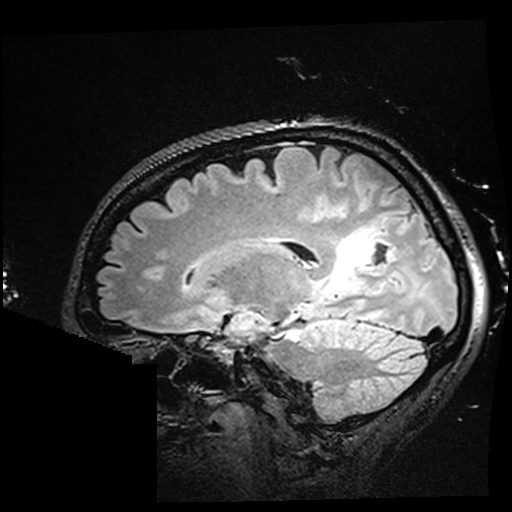
Brain MRI from a brain-tumour surgery series, one sagittal slice; T2 FLAIR; 512 × 512 image matrix. Case-level facts recorded for this patient, not image findings: histopathology: Oligodendroglioma; WHO grade: 2; IDH mutation: yes; tumour location: Right Parietal.
Annotated regions visible in this slice (manually delineated by an expert):
- residual tumour: box from (x=323, y=229) to (x=380, y=297) px